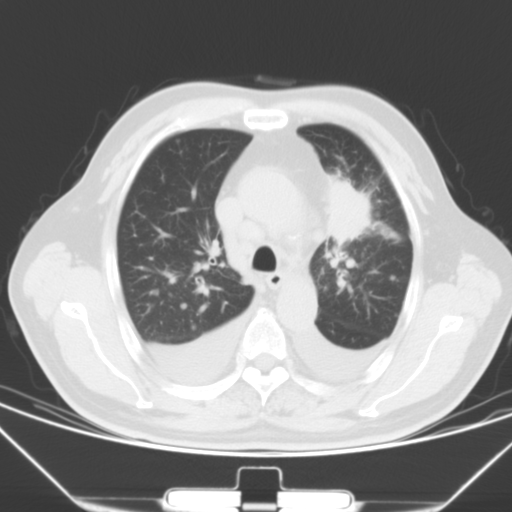
Chest CT, one axial slice. 120 kVp. Lung window (W 1500 / L -600 HU). 5 mm slice thickness. 512 × 512 image matrix, field of view 352 × 352 mm. Patient: male, 66 years. From the clinical record (not read from this slice): clinical TNM (as recorded): T1c N0 M0.
Structures marked on this image (bounding box drawn by a radiologist):
- lung tumour (recorded histology: adenocarcinoma): box from (x=316, y=167) to (x=370, y=253) px